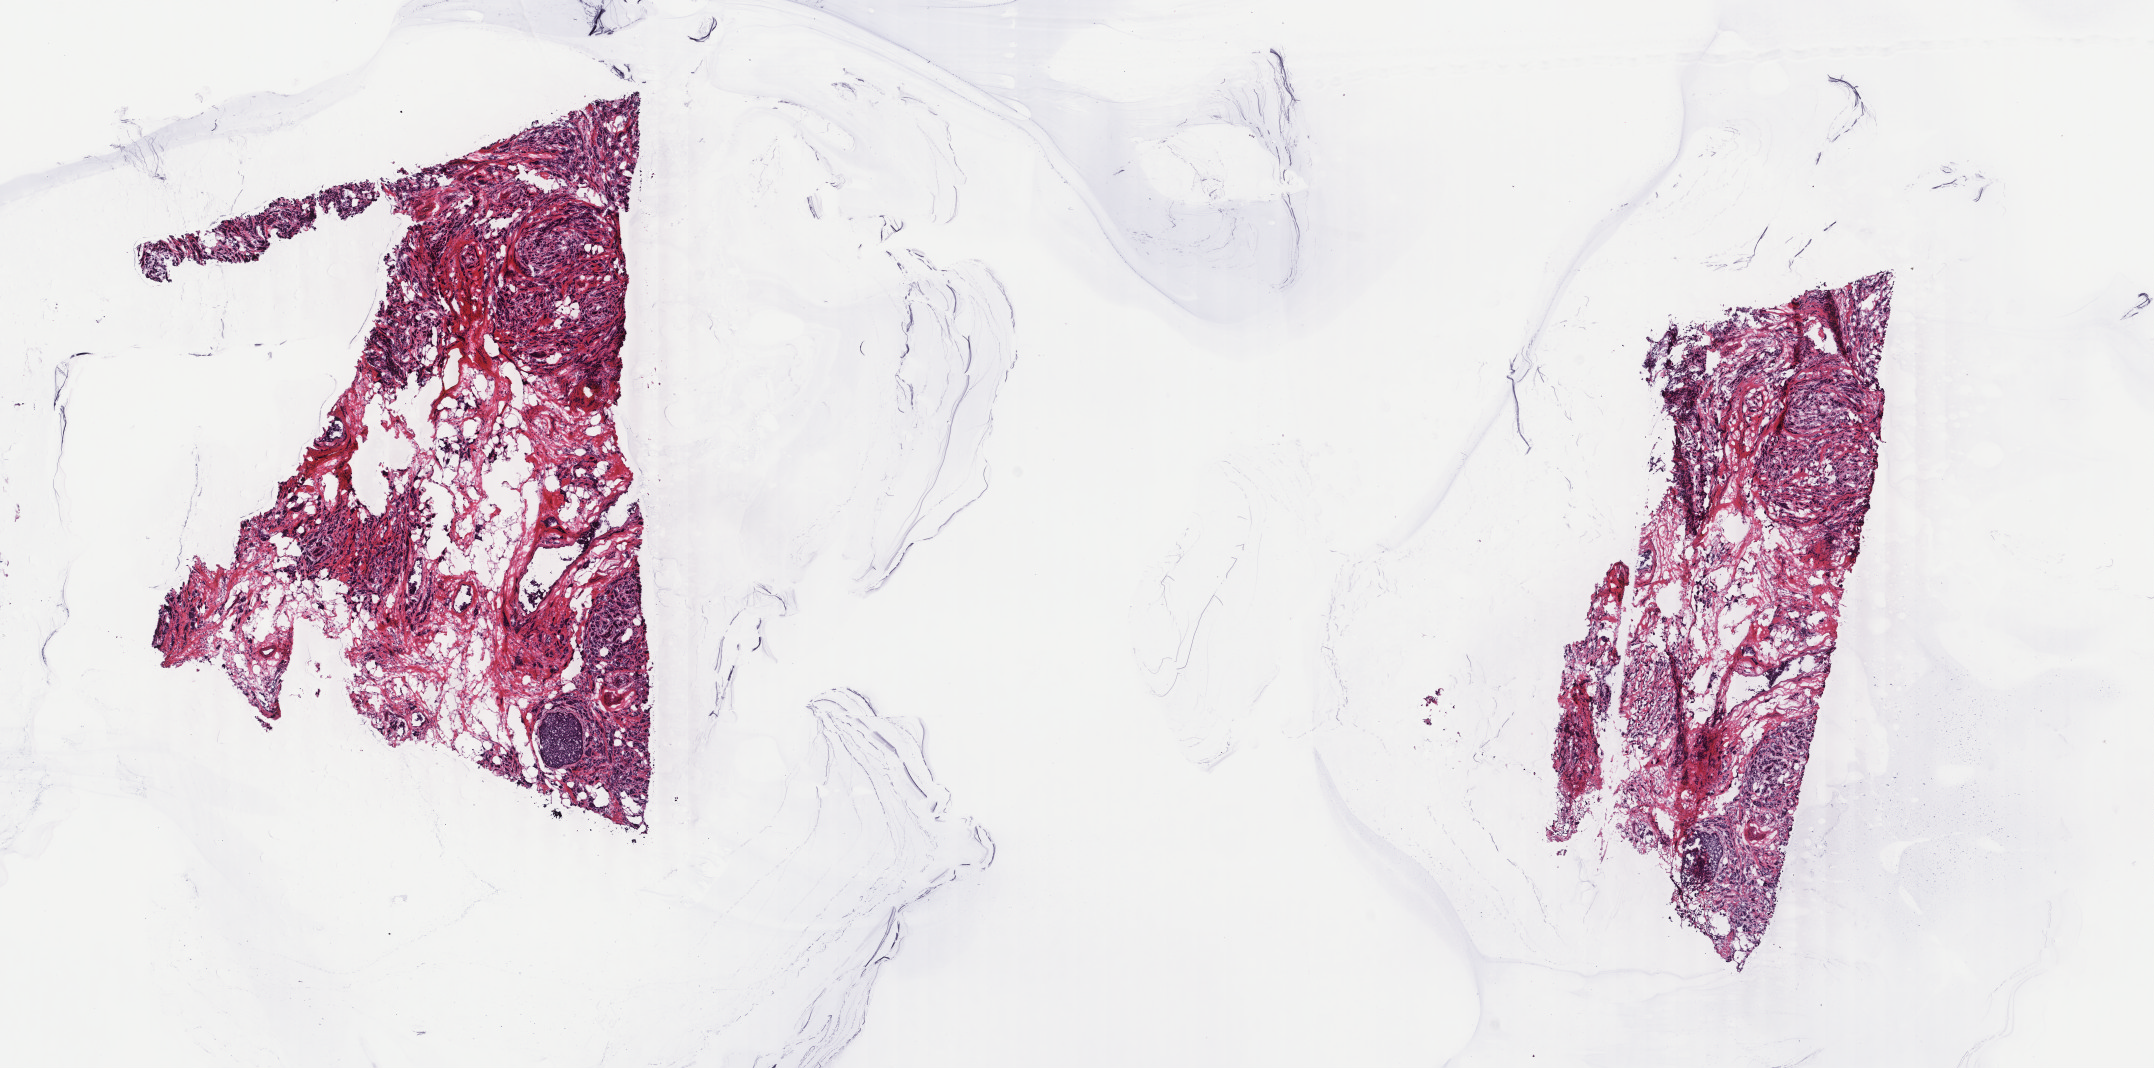
H&E-stained whole-slide image — shown as a low-resolution overview of the whole scanned area (about 17.1 x 8.5 mm); frozen section from the top of the tissue portion; sample: primary tumour, breast. Female, age 62 years at initial diagnosis. Pathologist review of this section (percent, as recorded): tumour cells 60%, tumour nuclei 75%, normal cells 10%, stromal cells 30%, necrosis 0%. Inflammatory infiltration, as recorded: lymphocyte infiltration 0%, monocyte infiltration 0%, neutrophil infiltration 0%.
• AJCC pathologic stage: IIIA (7th edition)
• laterality: right
• diagnosis: Infiltrating duct carcinoma, NOS